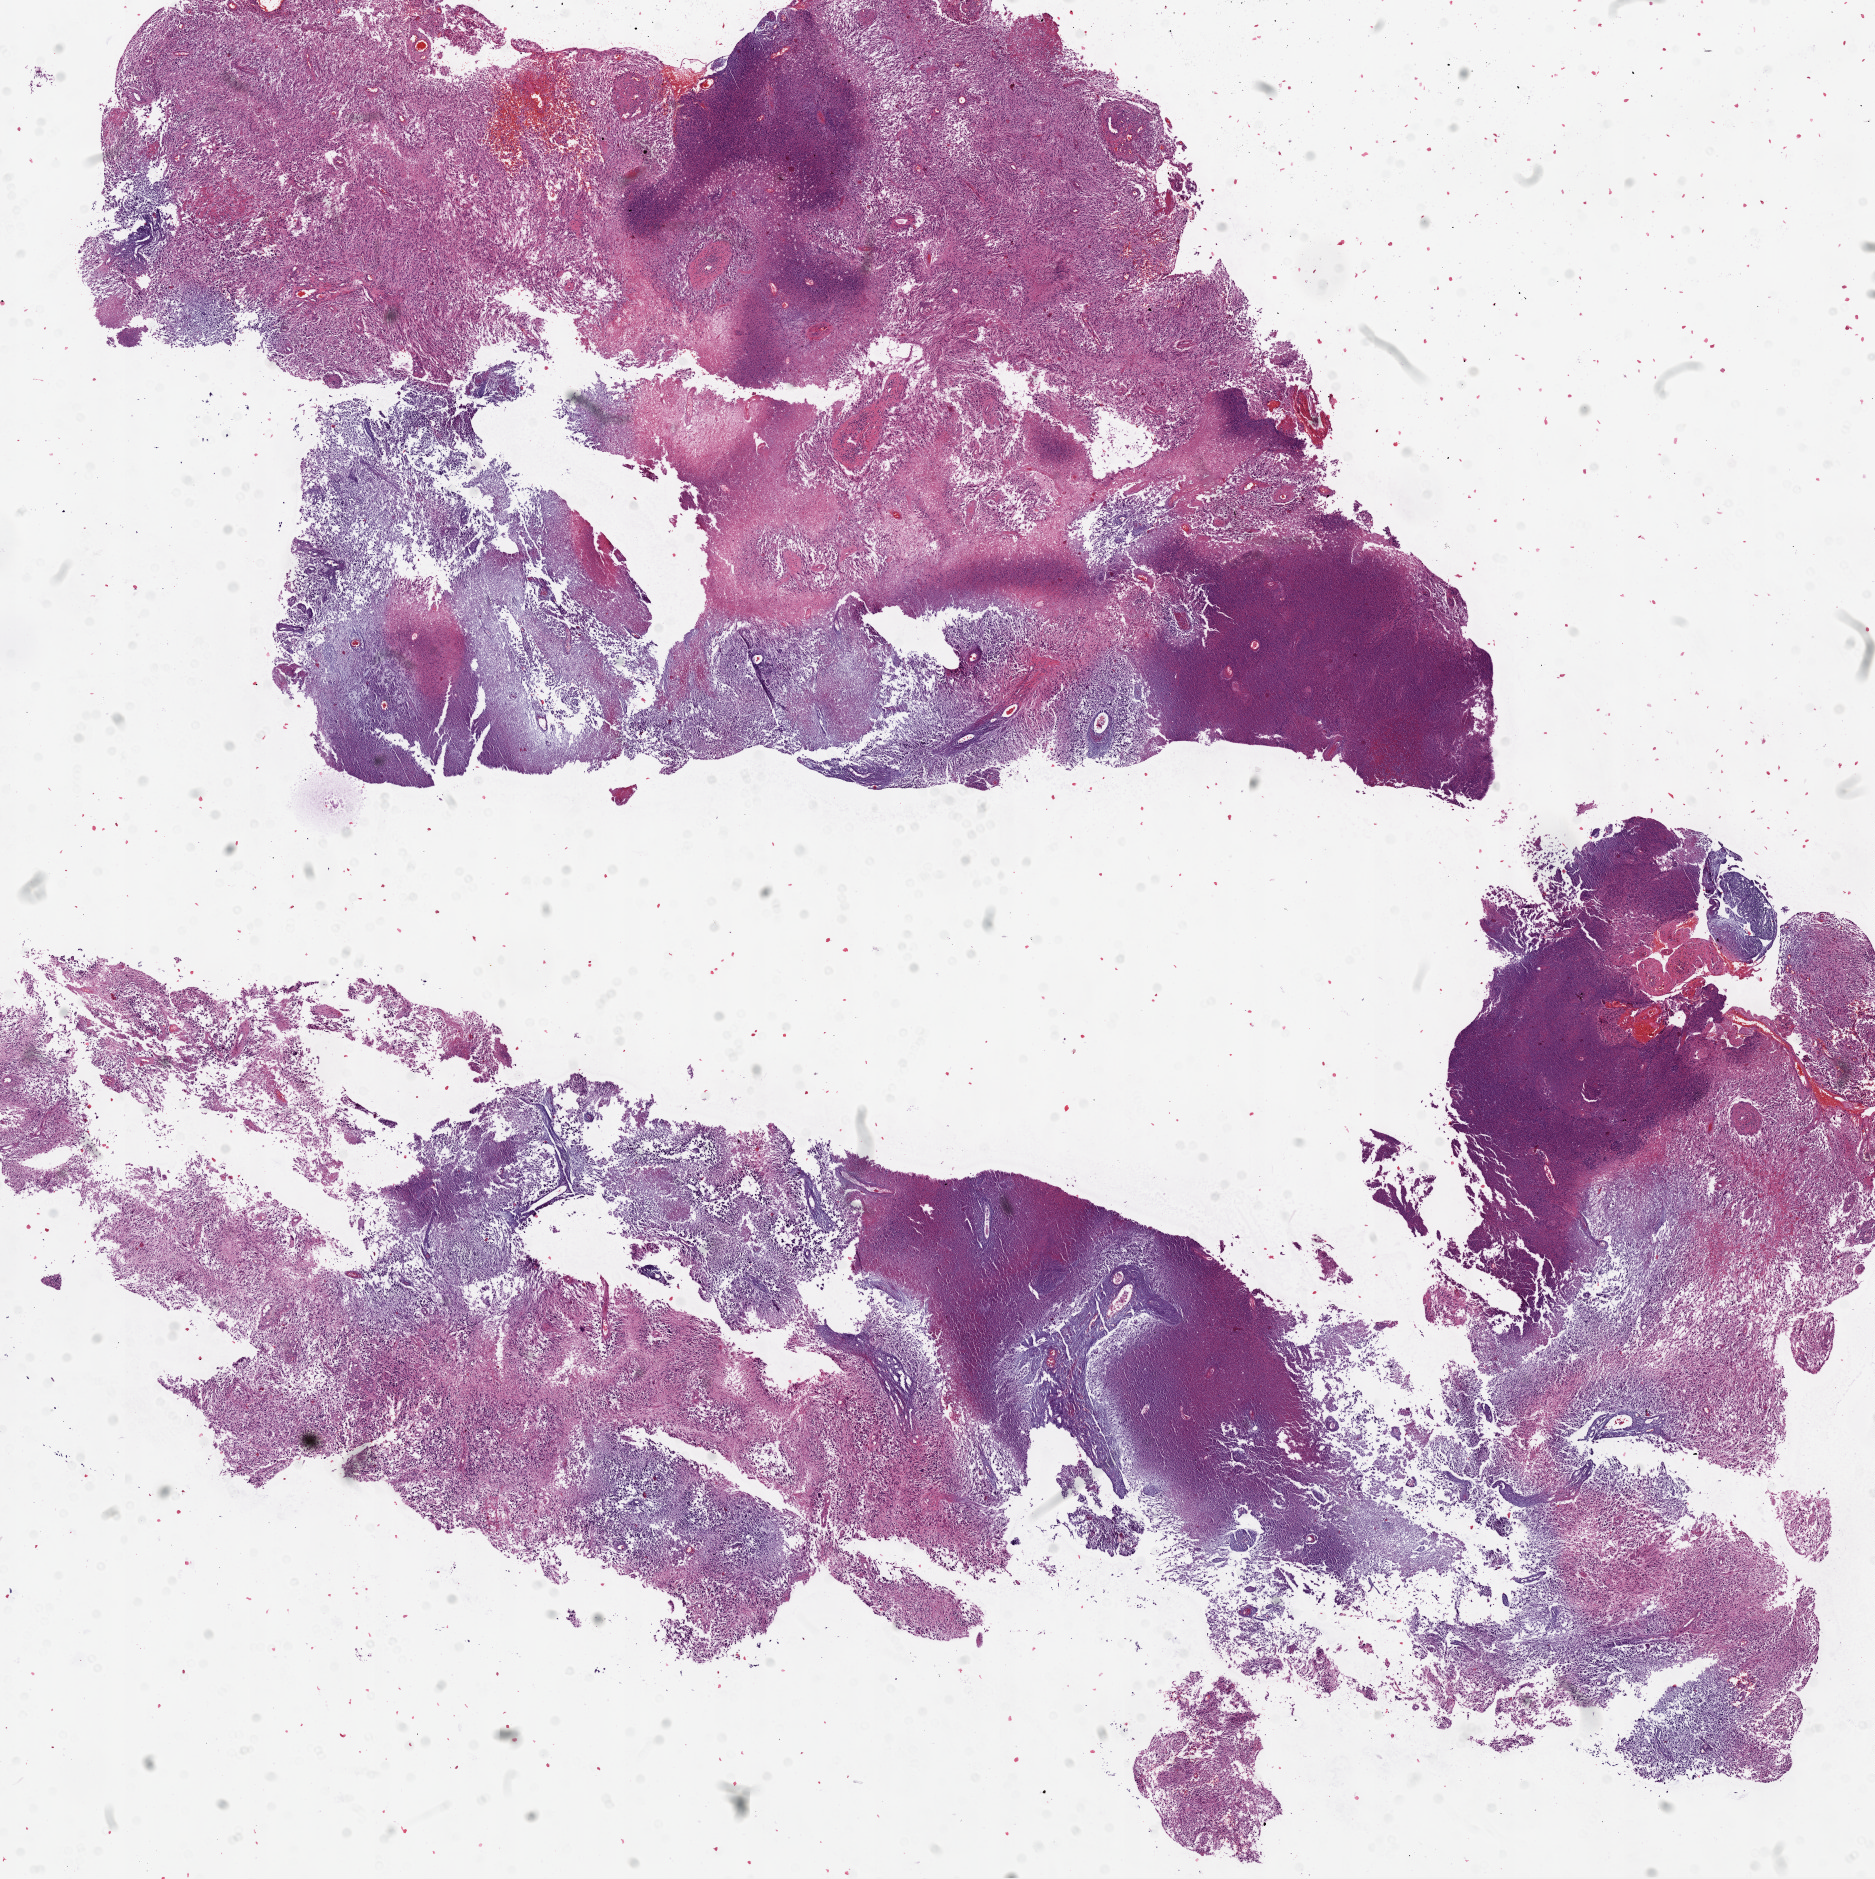
Digitized H&E tissue section (whole slide), whole scanned area (about 15.0 x 15.1 mm, acquisition: 20x scan) shown as a low-resolution overview; formalin-fixed paraffin-embedded (FFPE) diagnostic section; sample: primary tumour, brain. Male, age 74 years at initial diagnosis.
* histologic diagnosis: Glioblastoma